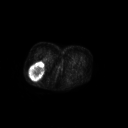
FDG PET of an extremity soft-tissue mass (from a PET/CT study), one axial slice. Slice 41 of 267 in the series (ordered by position). 3.27 mm slice thickness. 128 × 128 image matrix, field of view 700 × 700 mm. Female patient, age 70 years. From the clinical record (not read from this slice): histological type: synovial sarcoma; grade: intermediate; site of the primary tumour: right buttock.
Outlined on this slice (expert contour drawn on MRI and transferred to this co-registered scan by the dataset authors):
- gross tumour volume including surrounding oedema: box from (x=29, y=61) to (x=44, y=80) px
- gross tumour volume (mass): (x=29, y=61)–(x=44, y=80)